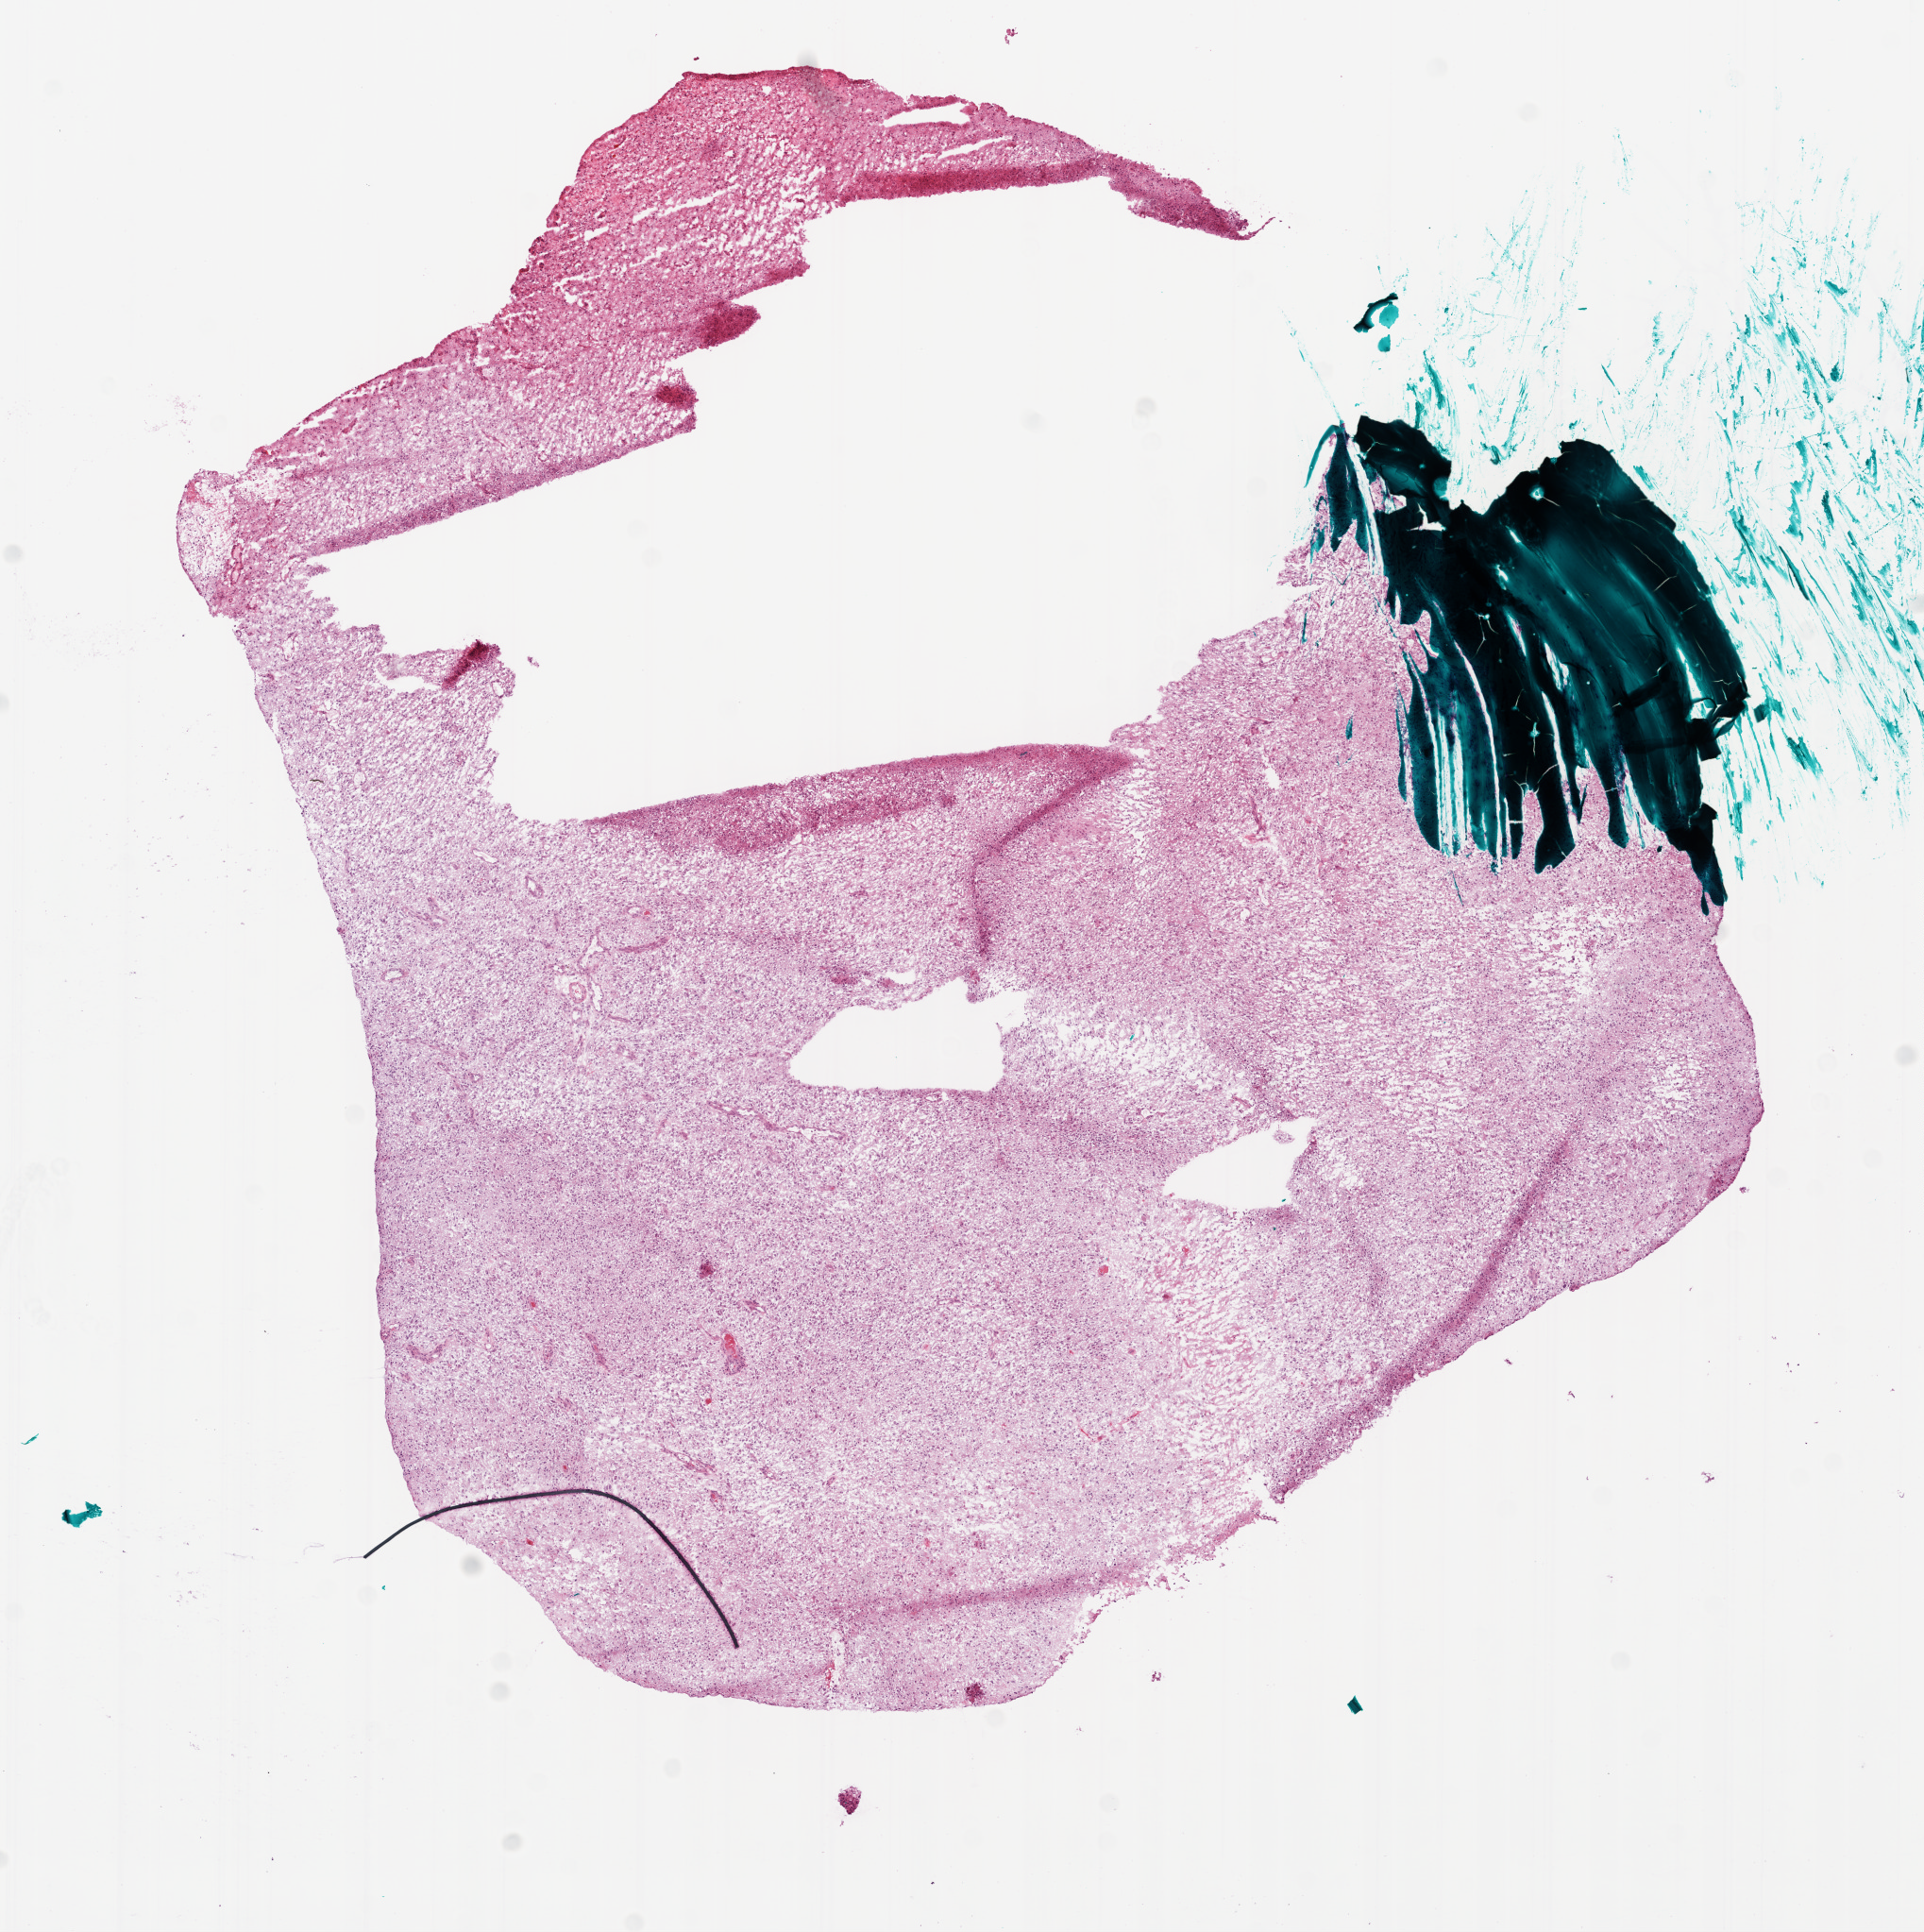
H&E whole-slide image, shown as a low-resolution overview of the whole scanned area (about 8.2 x 8.3 mm). Frozen section from the bottom of the tissue portion. Sample: primary tumour, brain. Male, age 57 years at initial diagnosis. Slide review estimates, as recorded: tumour cells 90%, tumour nuclei 100%, normal cells 0%, stromal cells 0%, necrosis 10%.
Pathologic diagnosis: Glioblastoma.